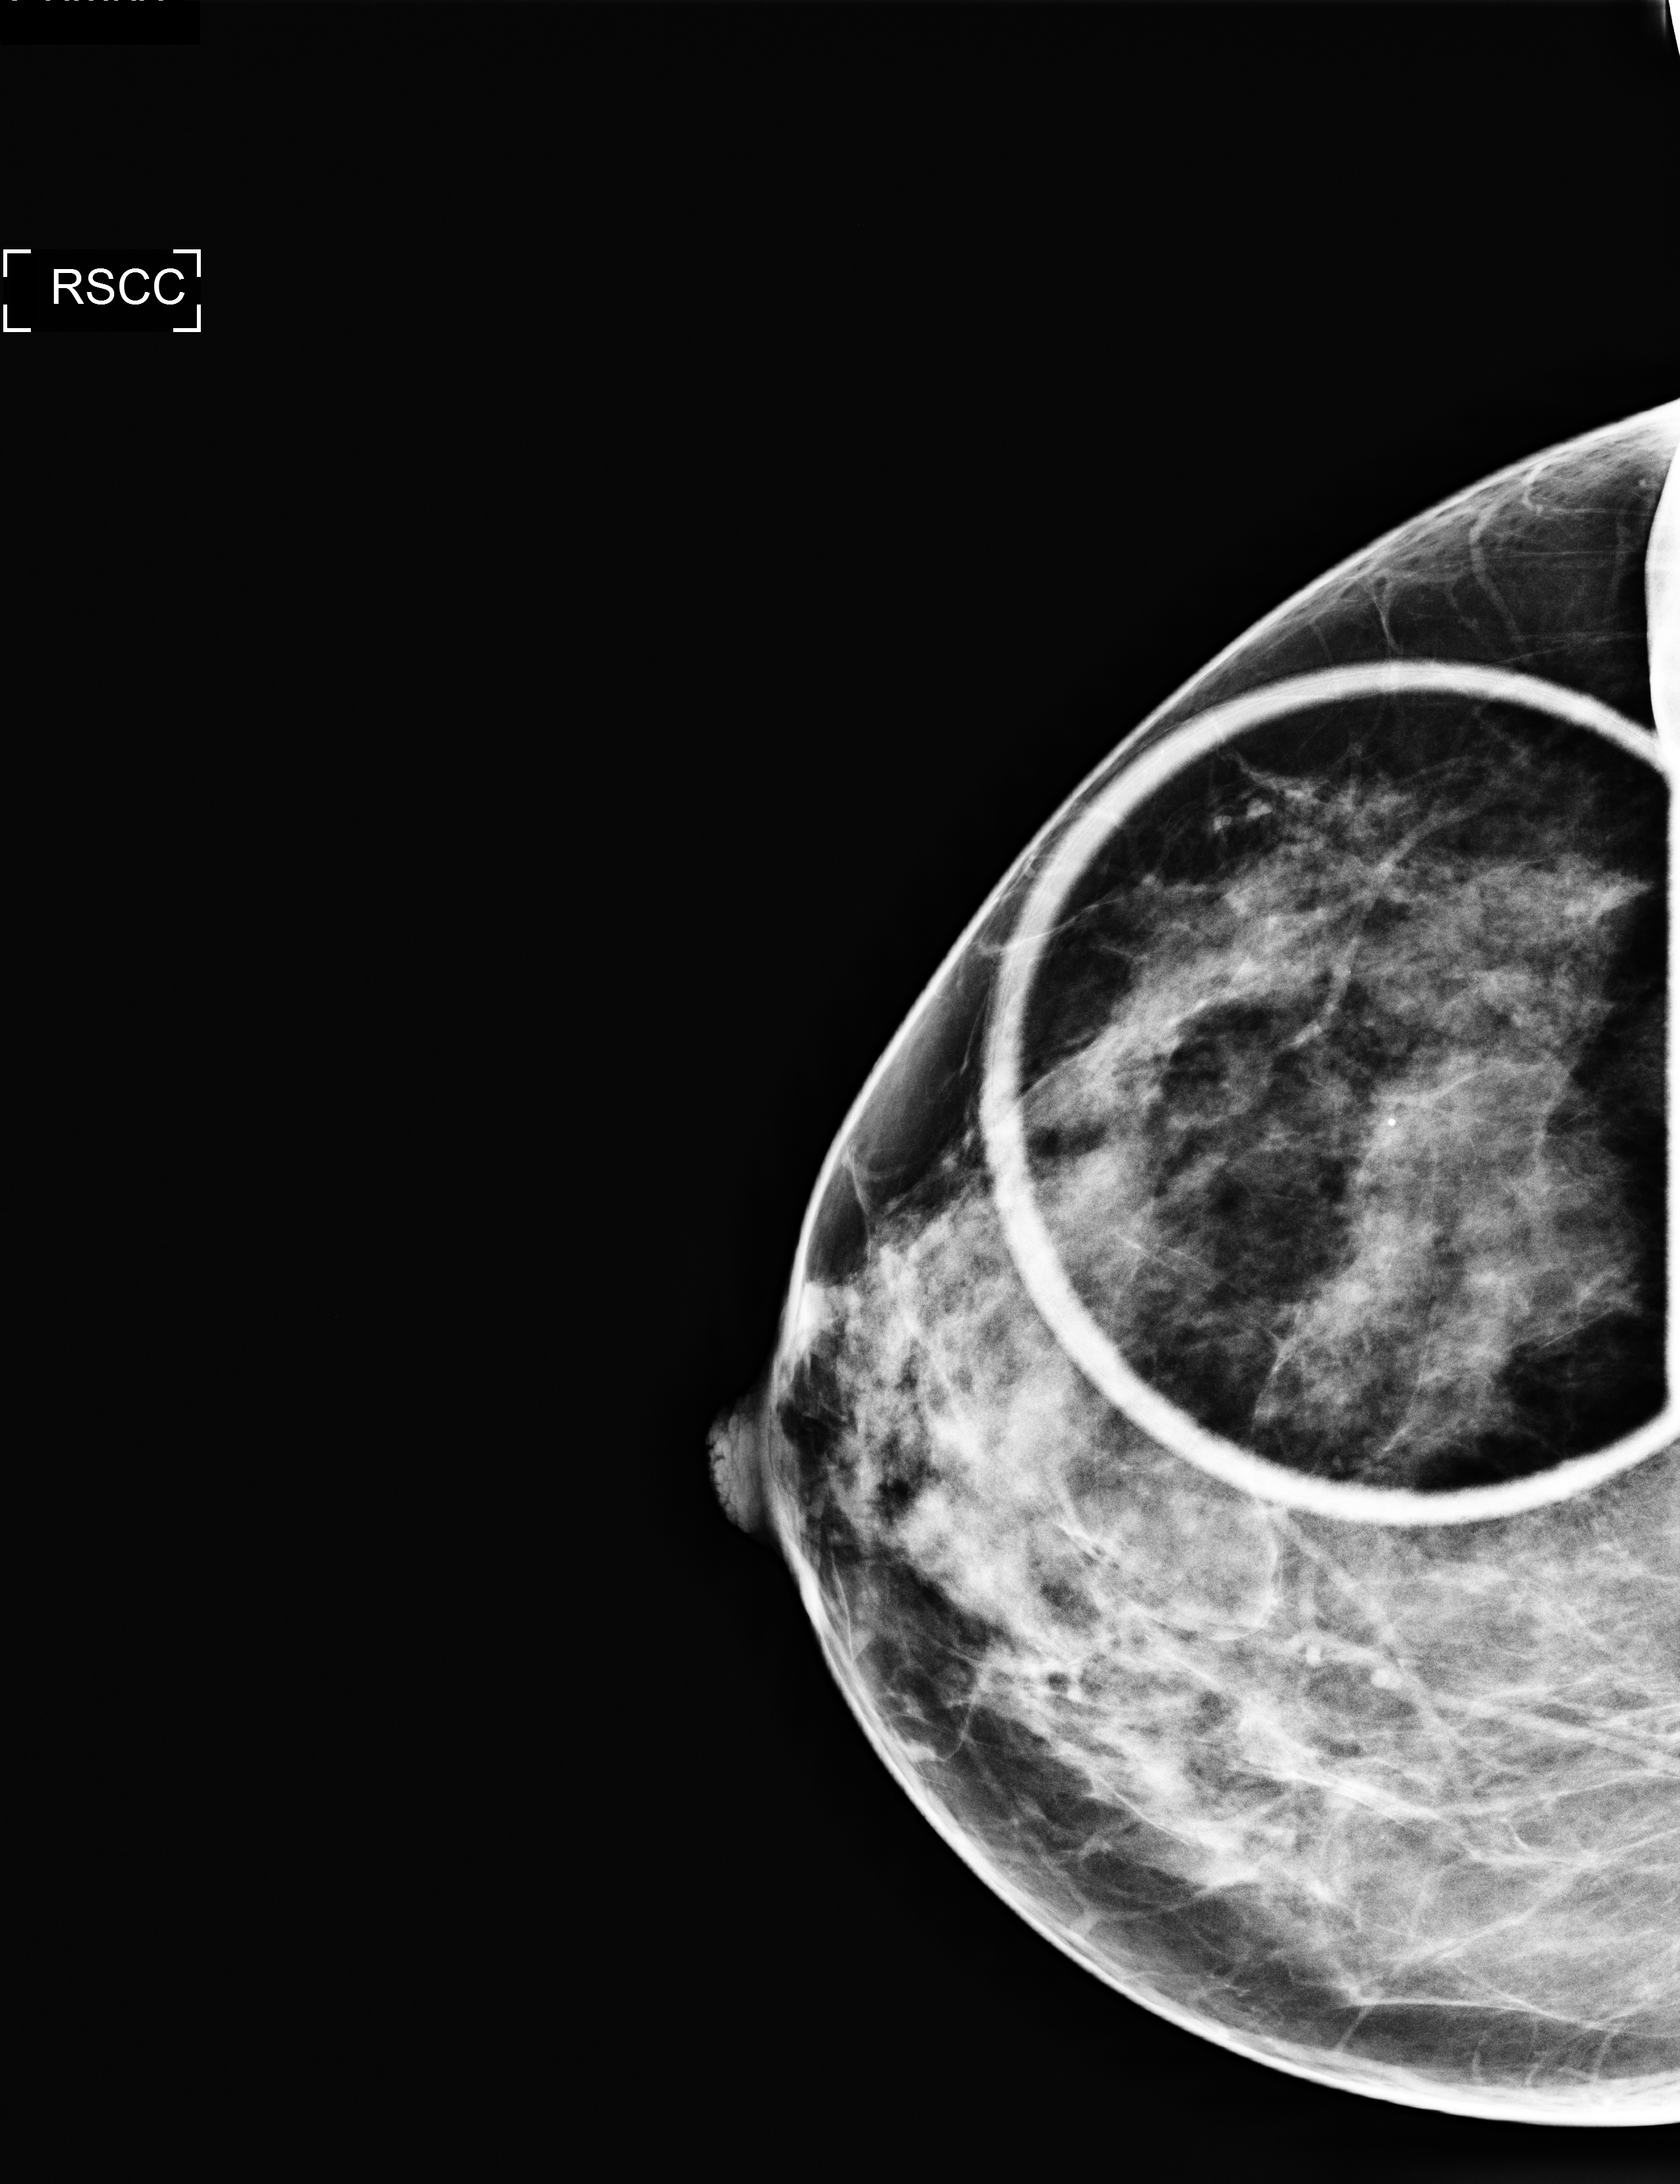
Additional work-up view, compressed breast thickness 43 mm, system: Selenia Dimensions. Female patient, age 41 years.
Image type: full-field digital mammogram. Breast: right. Projection: cranio-caudal projection, spot compression.